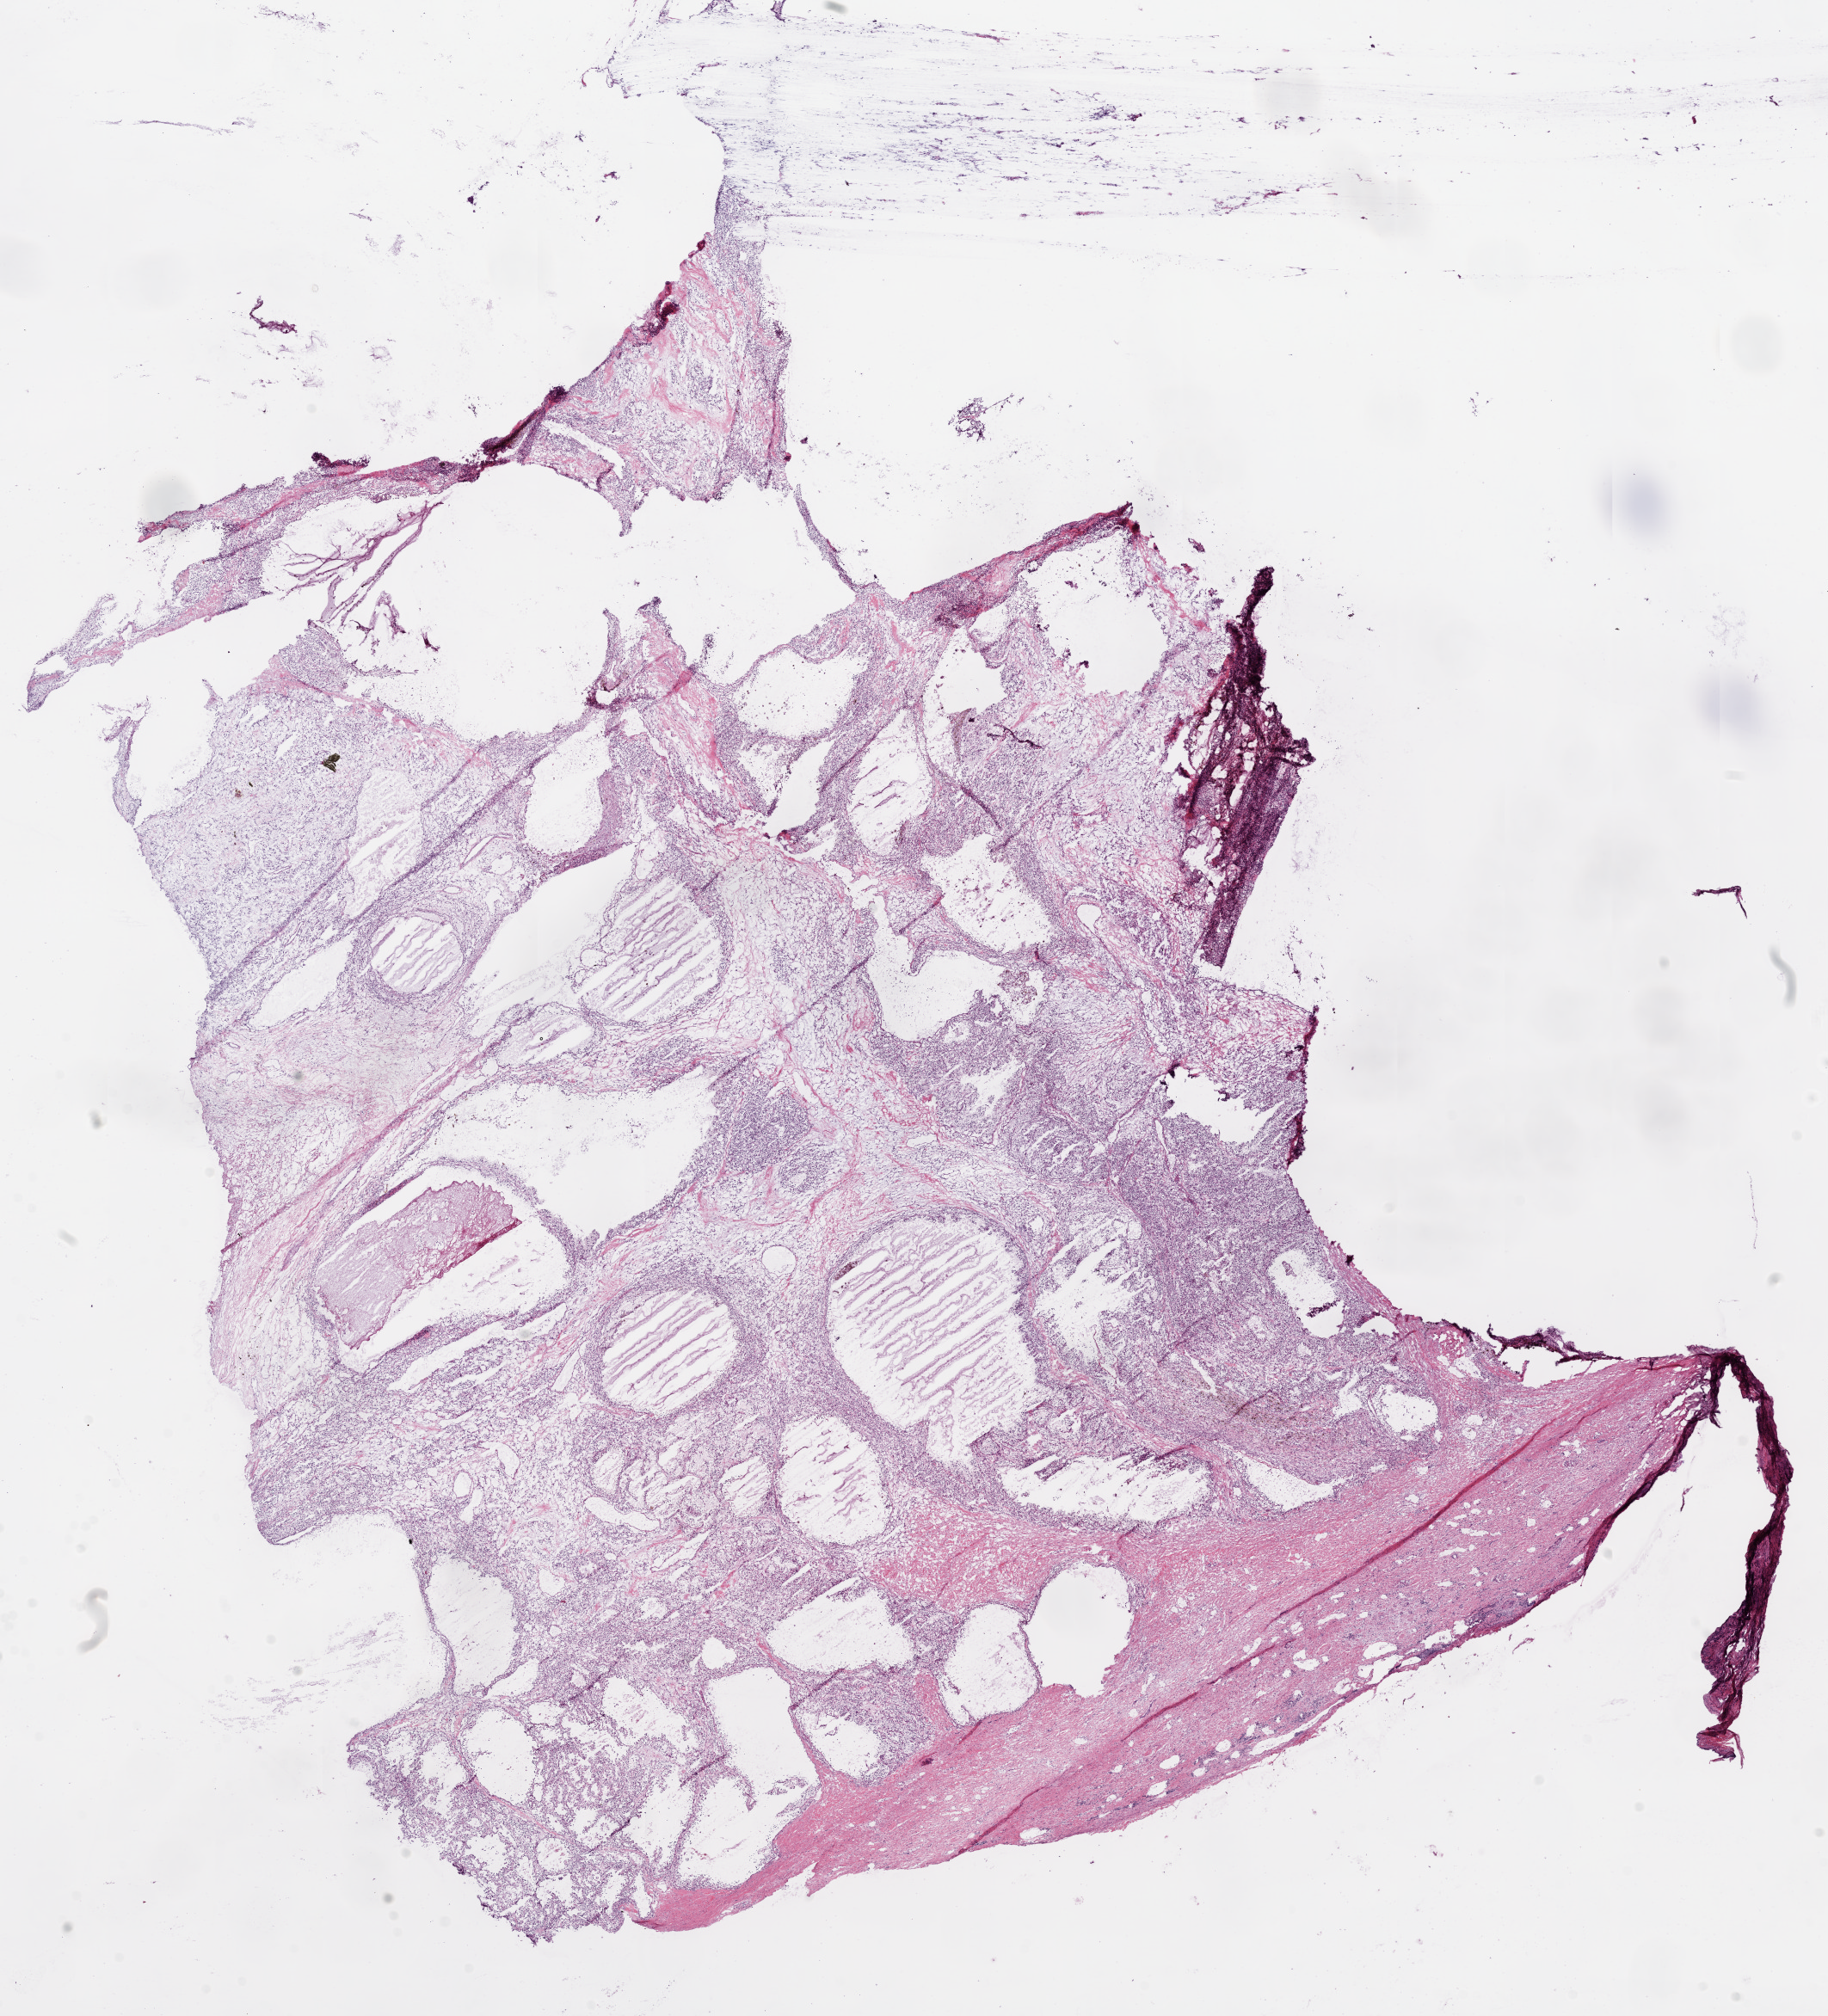
Digitized H&E tissue section (whole slide) — shown as a low-resolution overview of the whole scanned area (about 17.1 x 18.8 mm, slide scanned at 20x); frozen section; sample: primary tumour, kidney. Male patient; age at initial diagnosis 36 years. Slide review estimates, as recorded: tumour cells 65%, tumour nuclei 75%.
Diagnosis: Clear cell adenocarcinoma, NOS.